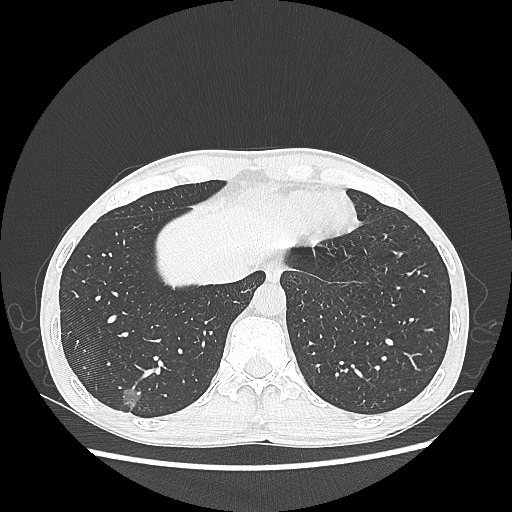
Chest CT, one axial slice; position 64 of 270 along the scan axis; 100 kVp; lung window (W 1500 / L -600 HU); 512 × 512 image matrix, field of view 360 × 360 mm. Male patient, age 60 years. From the clinical record (not read from this slice): clinical TNM (as recorded): T1c N0 M0; histopathological grade: G2.
Structures marked on this image (rectangle marked by the reading radiologist):
- lung tumour (recorded histology: adenocarcinoma): bounding box <114,382,148,418> (left, top, right, bottom; pixels)